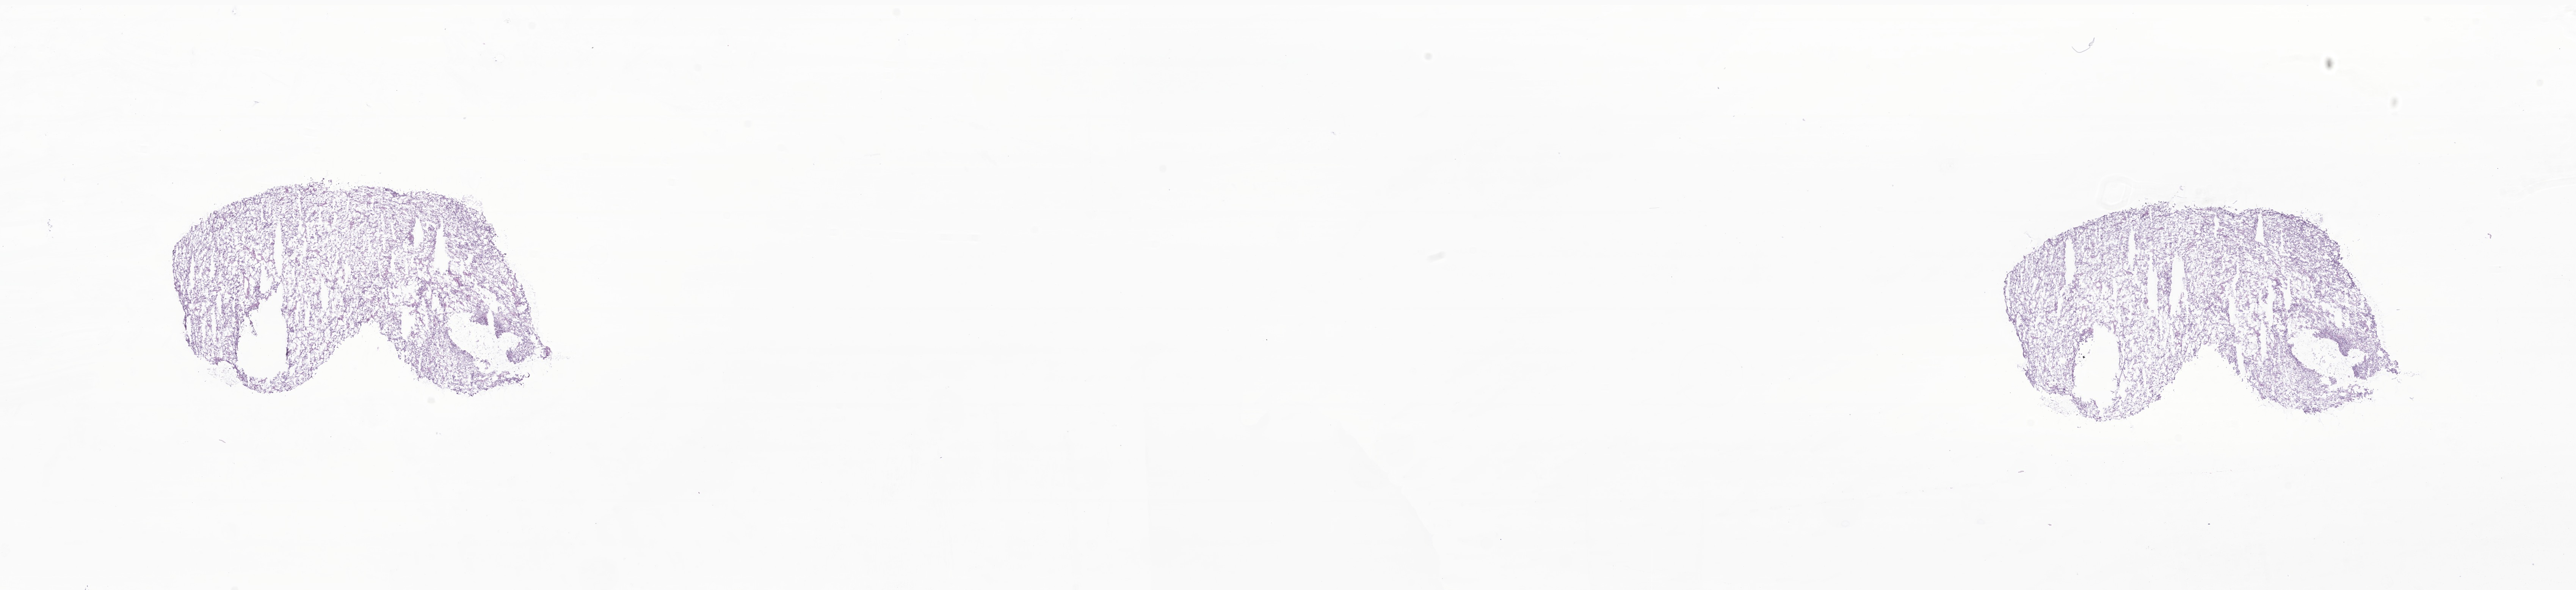
Whole-slide image, hematoxylin and eosin (H&E) stain of tumor tissue from the descended testis — shown as a low-resolution overview of the whole scanned area (about 28.6 x 6.6 mm). Frozen section. Patient male; age 183 months.
Diagnosis: Embryonal rhabdomyosarcoma, NOS.